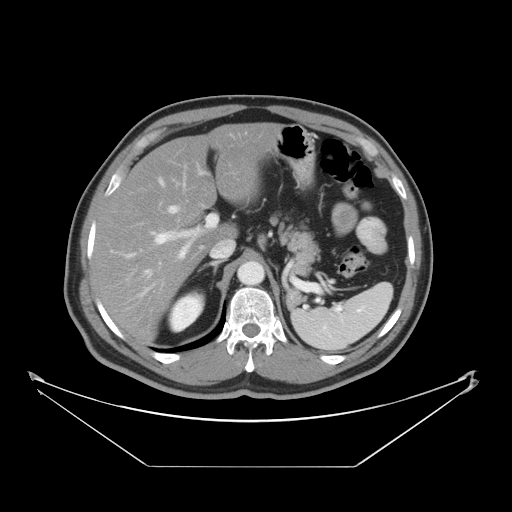
Contrast-enhanced abdominal CT, one axial slice. Reconstruction kernel STANDARD. 120 kVp. Intravenous contrast given. Soft-tissue window (W 400 / L 40 HU). 512 × 512 image matrix, field of view 465 × 465 mm. Male patient, age 57 years. Case-level facts recorded for this patient, not image findings: diagnosis: colorectal cancer liver metastases, imaged before liver resection; multiple liver metastases: no; largest metastasis: 3.3 cm; disease in both lobes: no.
Structures marked on this image (manually delineated by an expert):
- hepatic veins: bounding box [x1, y1, x2, y2] px = [158, 178, 180, 214]
- liver: [92, 125, 275, 341]
- planned liver remnant (the part of the liver to remain after resection): [92, 125, 275, 341]
- portal vein (with intrahepatic branches): [130, 214, 218, 299]